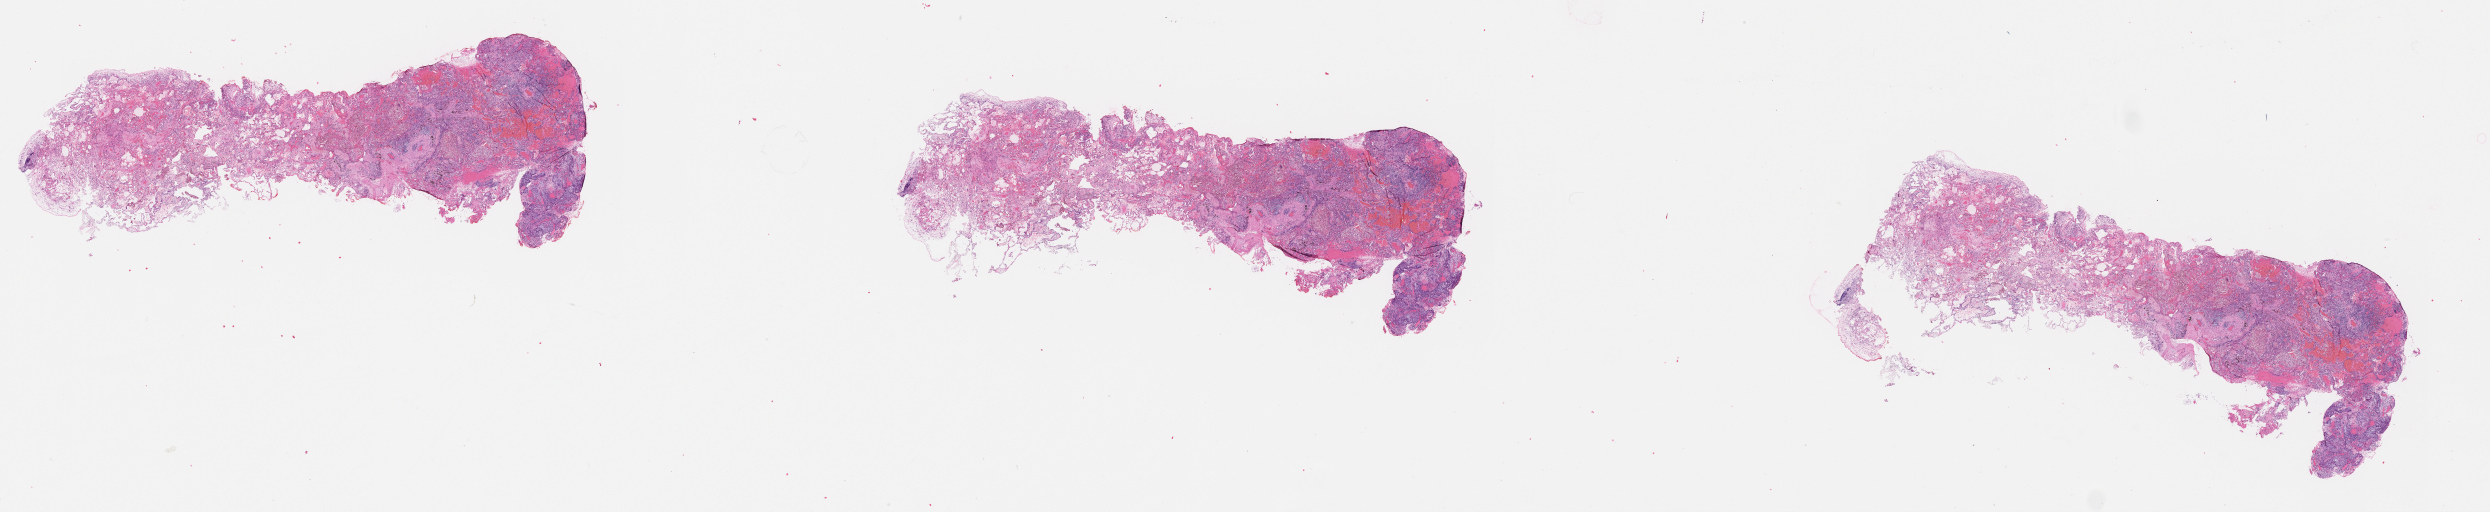
H&E whole-slide image — shown as a low-resolution overview of the whole scanned area (about 40.1 x 8.2 mm, acquisition: 20x scan). Lung, normal (non-tumour) tissue. Patient: male, age 57 years.
* this section: normal (non-tumour) tissue from the same patient
* patient diagnosis (cohort enrolment): squamous cell carcinoma (lung)